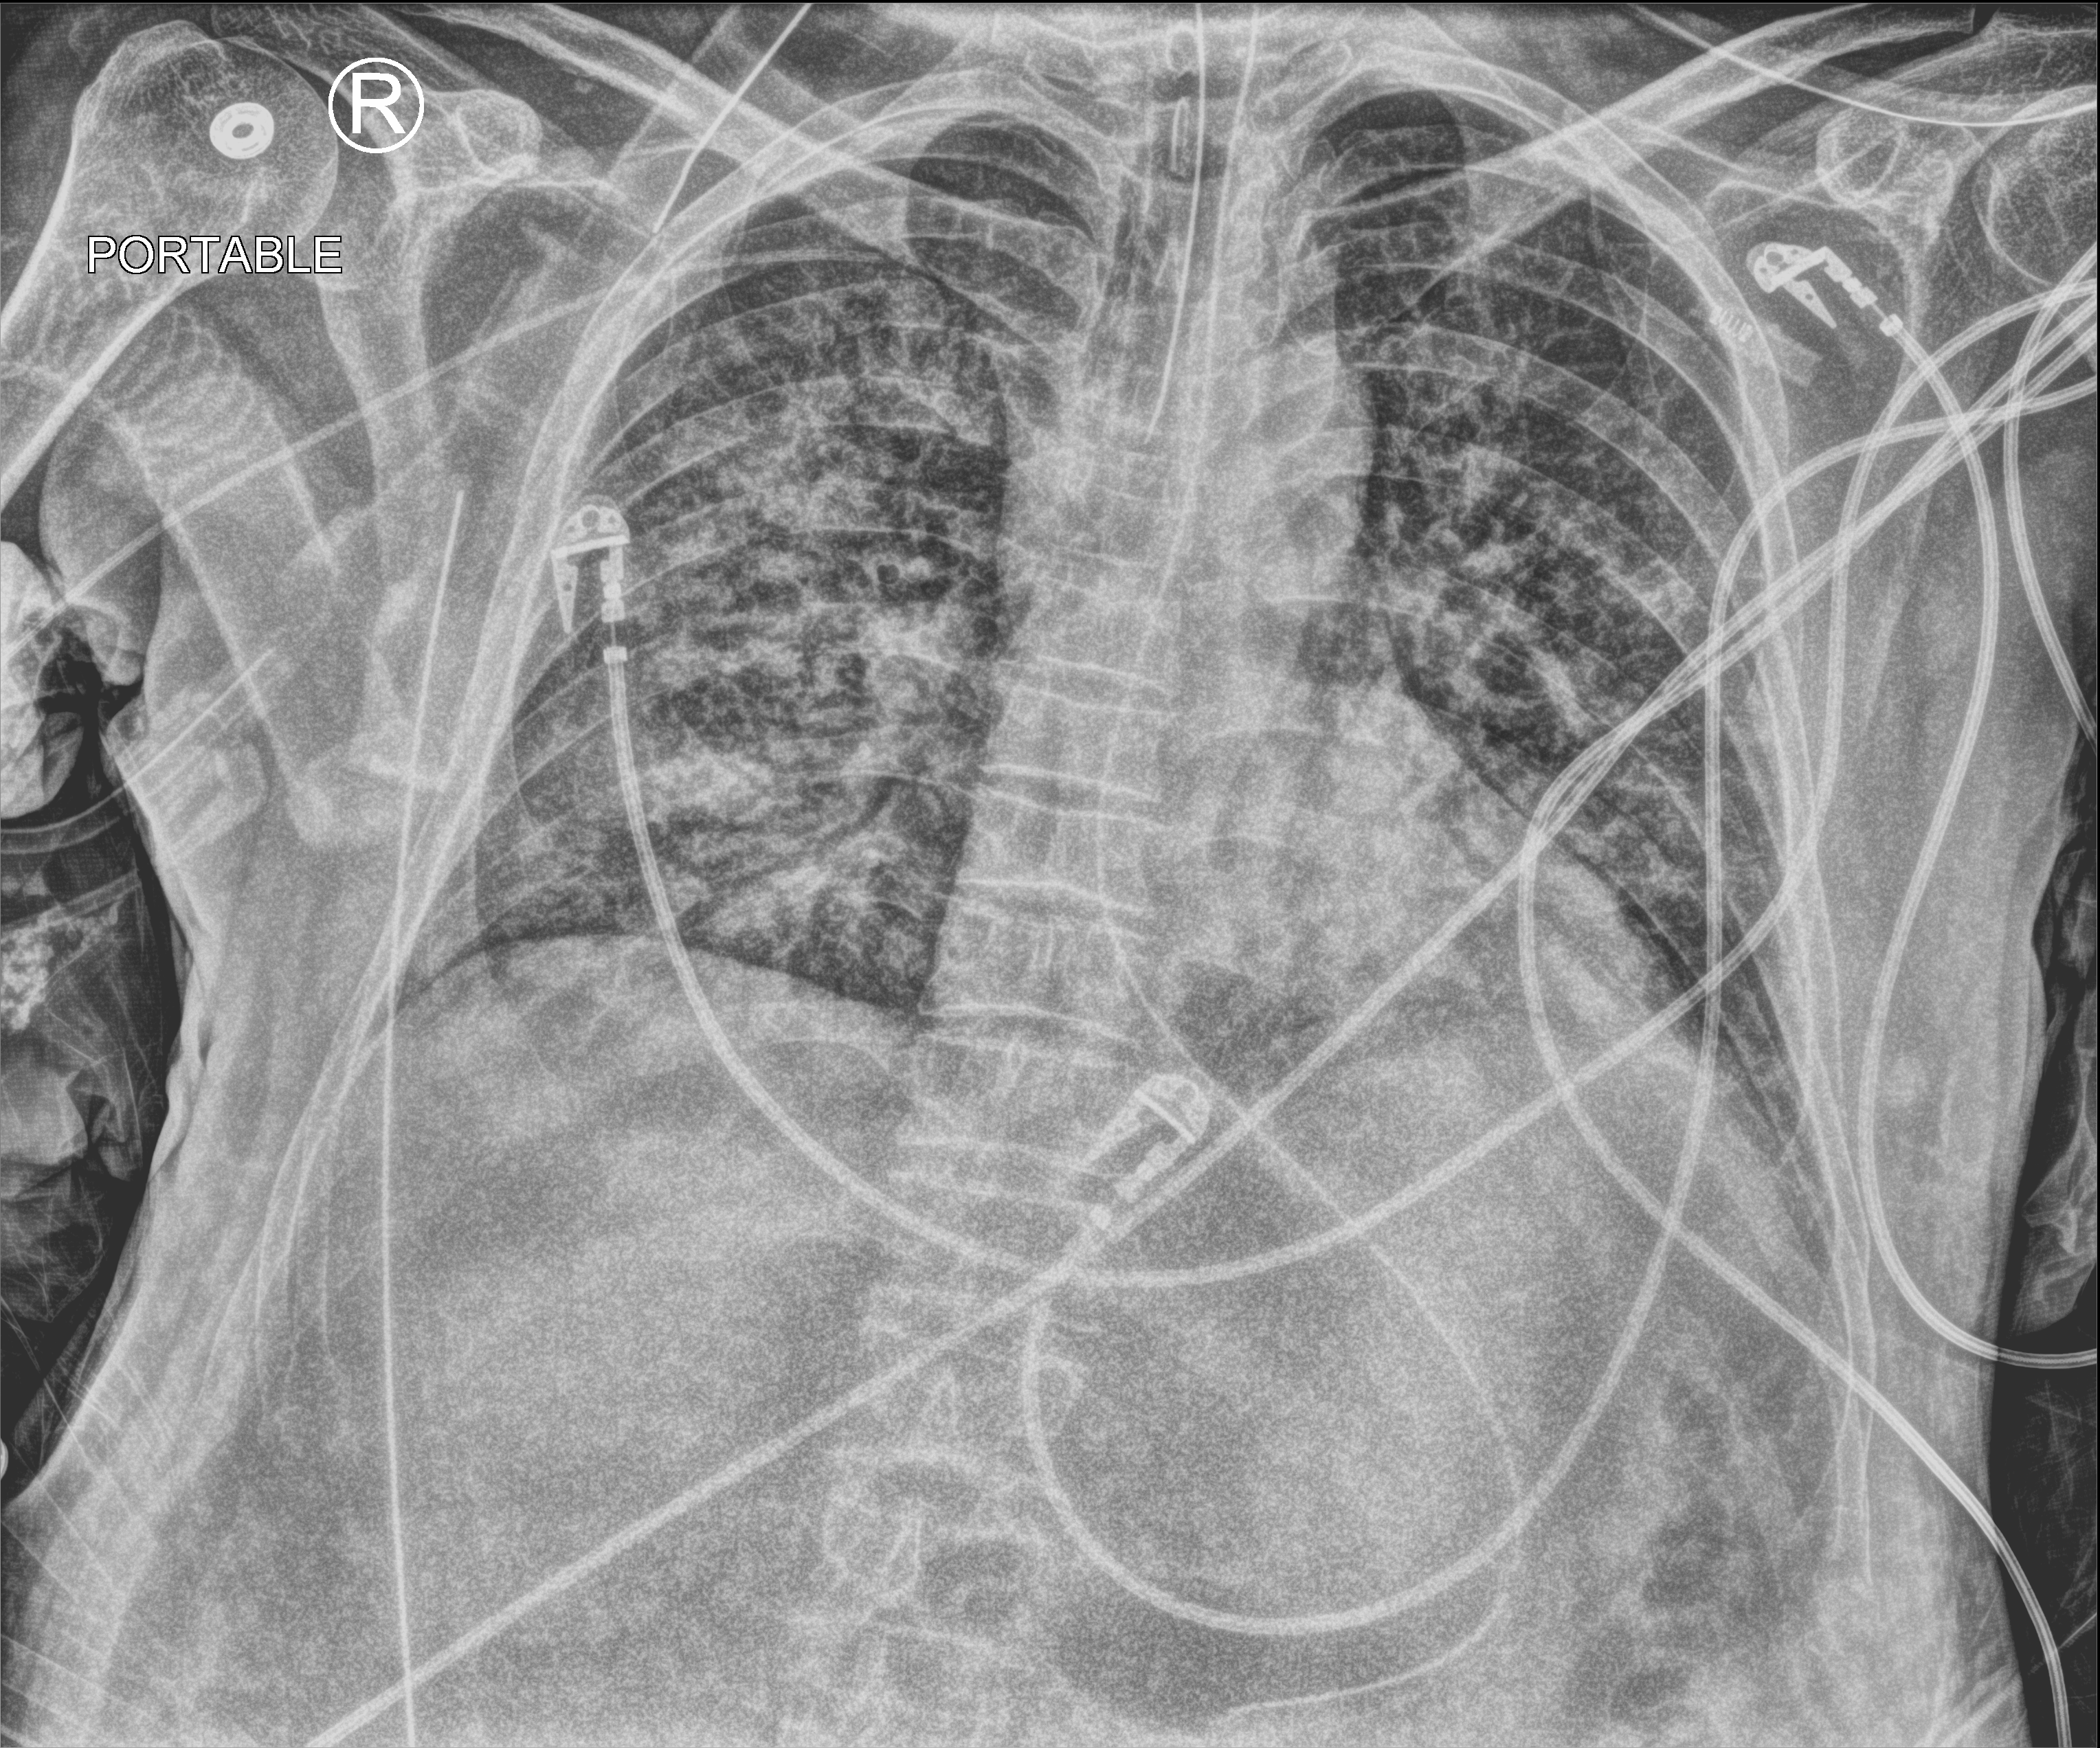
Chest X-ray (portable), anteroposterior (AP) projection. Patient hospitalised with COVID-19; male, aged 60–74 years.
Hospital-stay facts (about this admission, not read from this image; timing relative to this image not recorded): length of hospital stay: 19 days; admitted to intensive care during this hospital stay: yes.